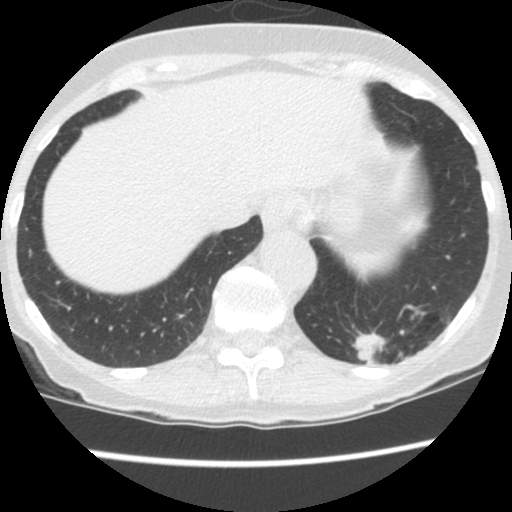
Low-dose screening chest CT, one axial slice. Position 28 of 130 along the scan axis. Reconstruction kernel STANDARD. 120 kVp. Lung window (W 1500 / L -600 HU). 2.5 mm slice thickness. 512 × 512 image matrix, field of view 290 × 290 mm.
Annotated regions visible in this slice (expert manual segmentation):
- lesion 1 (tumor, lower lobe of left lung): box from (x=351, y=329) to (x=390, y=366) px